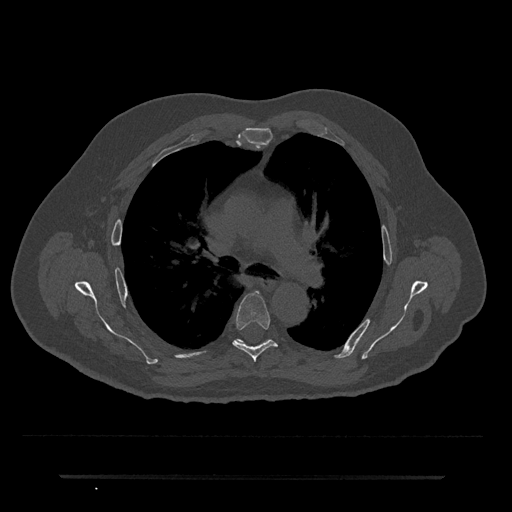
CT including the spine, one axial slice. Position 478 of 797 along the scan axis. Reconstruction kernel Br40s/3. 120 kVp. Bone window (W 1800 / L 400 HU). 0.5 mm slice thickness. 512 × 512 image matrix, field of view 437 × 437 mm. Patient: male, 69 years. Case-level facts recorded for this patient, not image findings: primary cancer: prostate.
Annotated regions visible in this slice (semi-automatically segmented with operator editing):
- T5 vertebra: bounding box [x1, y1, x2, y2] px = [233, 291, 278, 362]